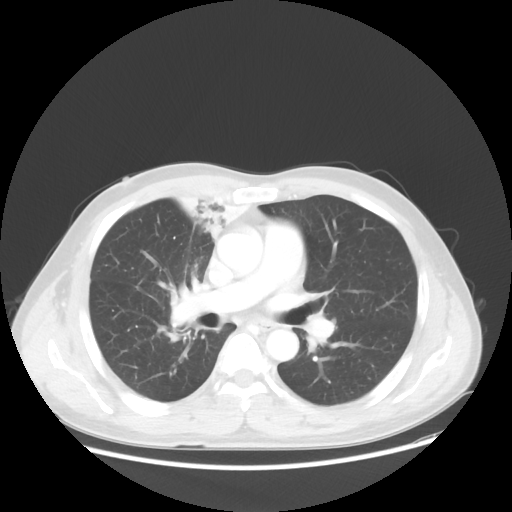
Chest CT, one axial slice; slice 31 of 56 in the series (ordered by position); reconstruction kernel STANDARD; lung window (W 1500 / L -600 HU); 512 × 512 image matrix, field of view 398 × 398 mm. Male patient, age 60 years. Case-level facts recorded for this patient, not image findings: clinical TNM (as recorded): T2a N1 M0.
Outlined on this slice (rectangle marked by the reading radiologist):
- lung tumour (recorded histology: squamous cell carcinoma): bounding box [x1, y1, x2, y2] px = [168, 183, 261, 253]